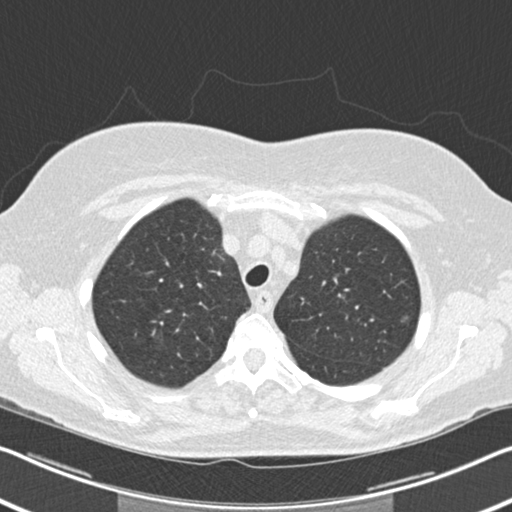
Chest CT (low-dose screening protocol), one axial image, second annual screen, lung window (W 1500 / L -600 HU), 2 mm slice thickness, standard (soft-tissue) reconstruction kernel (B30f), 512 × 512 image matrix, field of view 336 × 336 mm. Female participant, aged 60 years at enrolment.
- Lesion marked by an expert reader, box from (x=388, y=305) to (x=428, y=341) px.
- The screening reader recorded 6 non-calcified nodules or masses ≥4 mm on this exam (right upper lobe, right middle lobe, right lower lobe, right lower lobe, left lower lobe, lingula); which of them this box marks is not recorded.